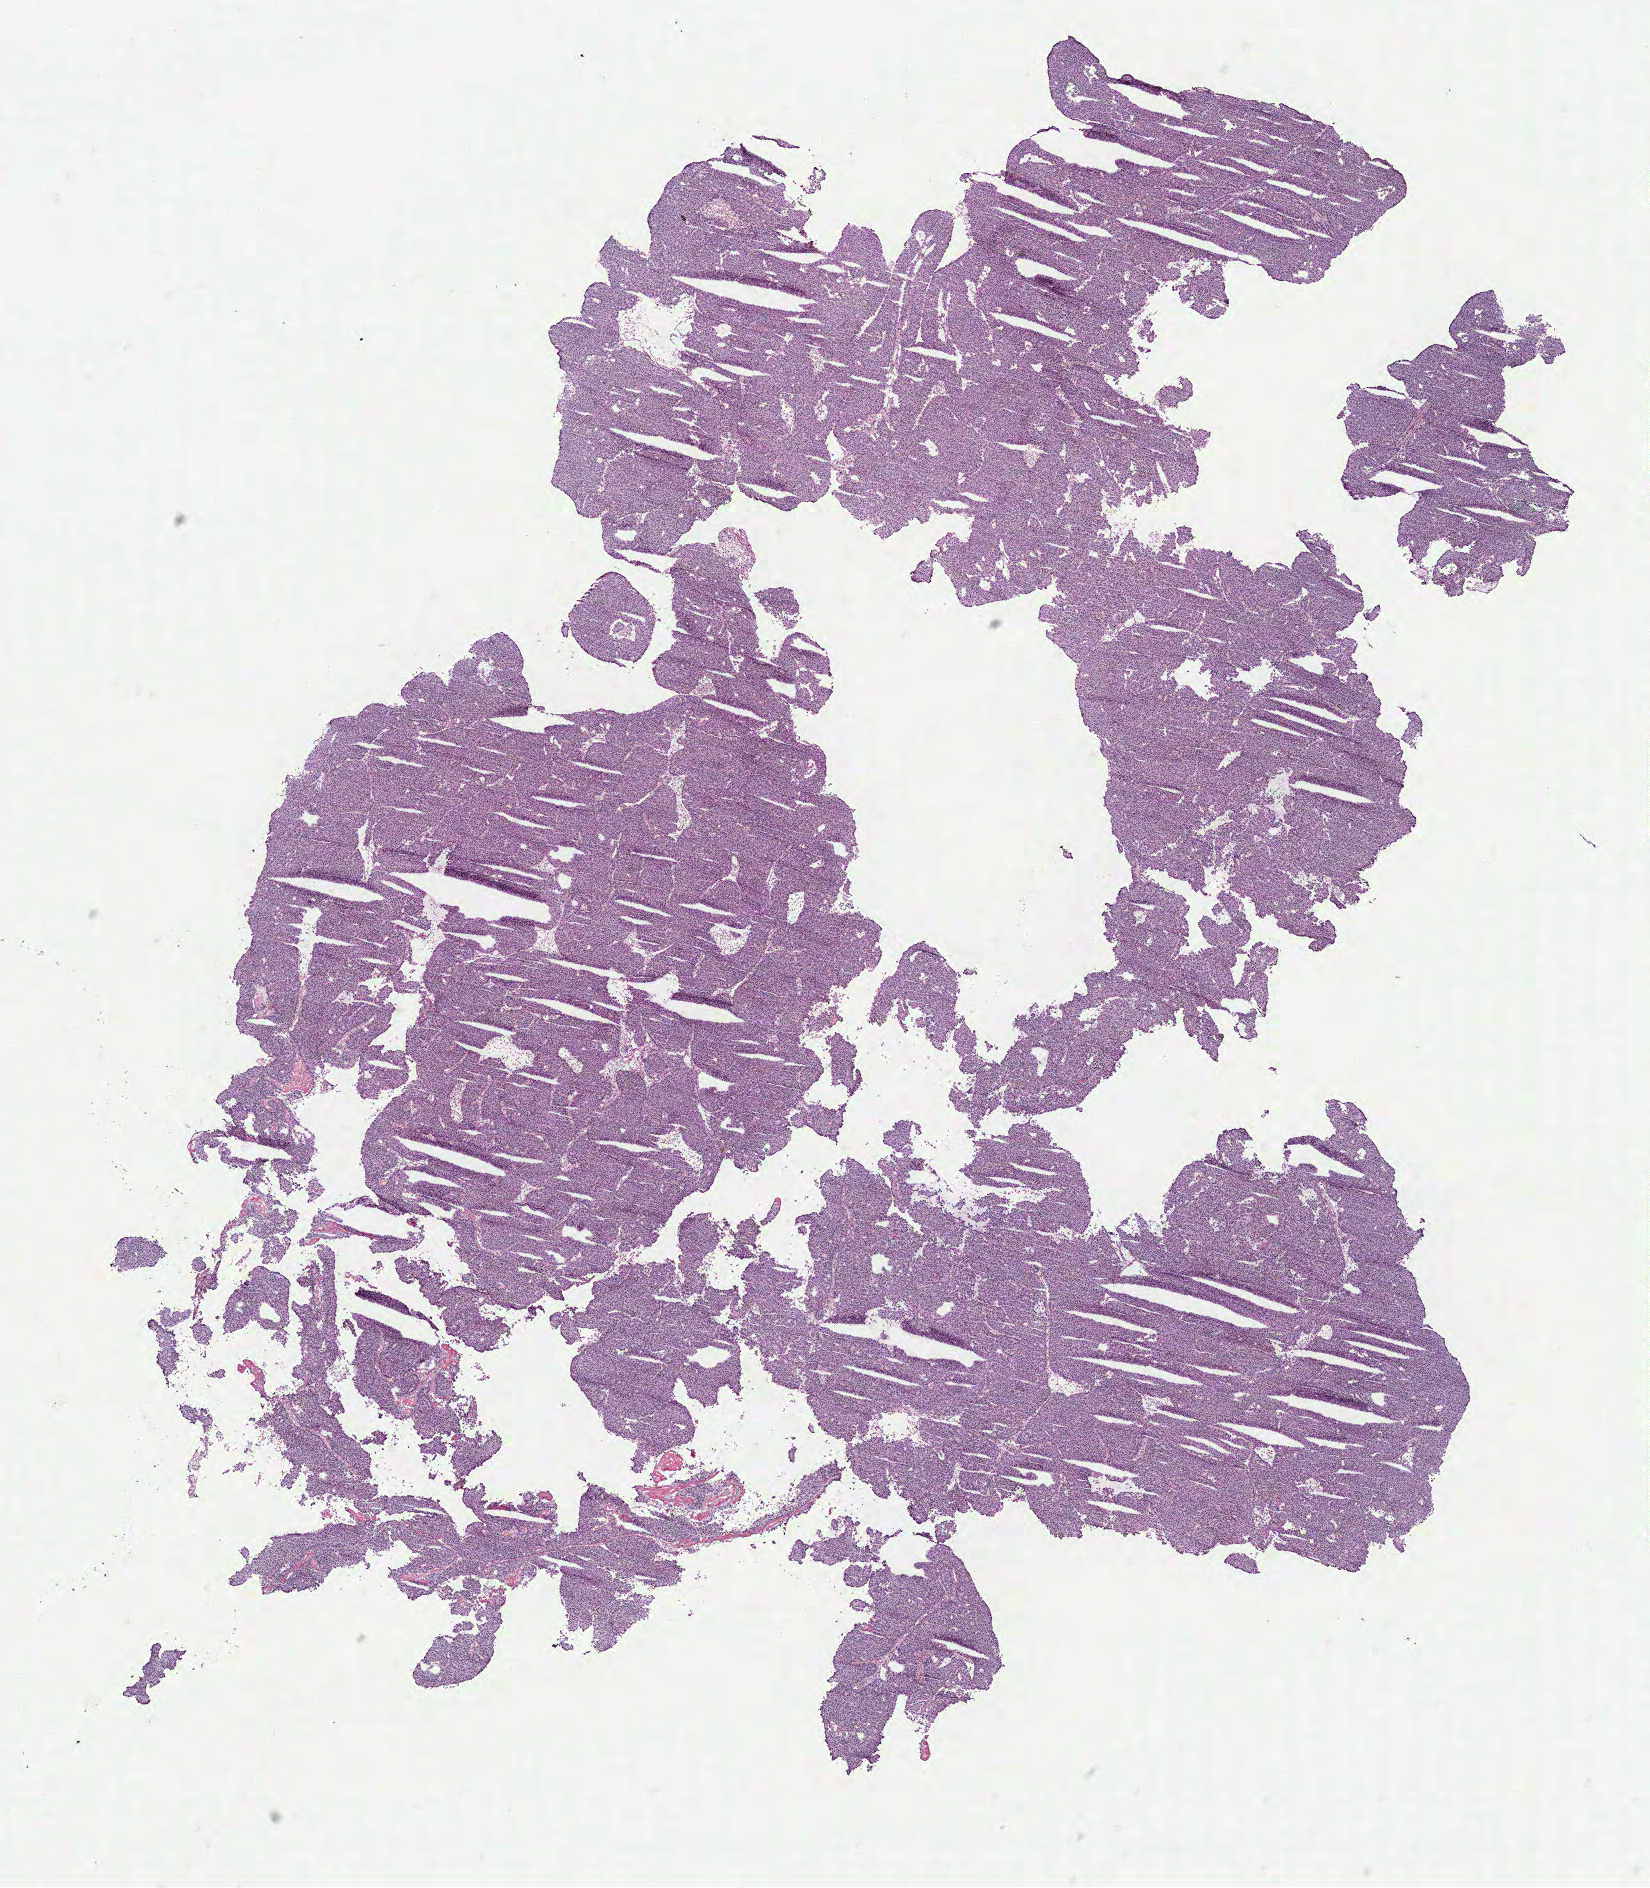
Digitized H&E-stained tissue section (whole slide) — low-resolution overview of the scanned area, about 13.2 x 15.1 mm (slide scanned at 40x), tumour tissue sample, breast. Female, 46 y/o.
Diagnosis: Infiltrating duct carcinoma, NOS. AJCC pathologic stage: IIIB.